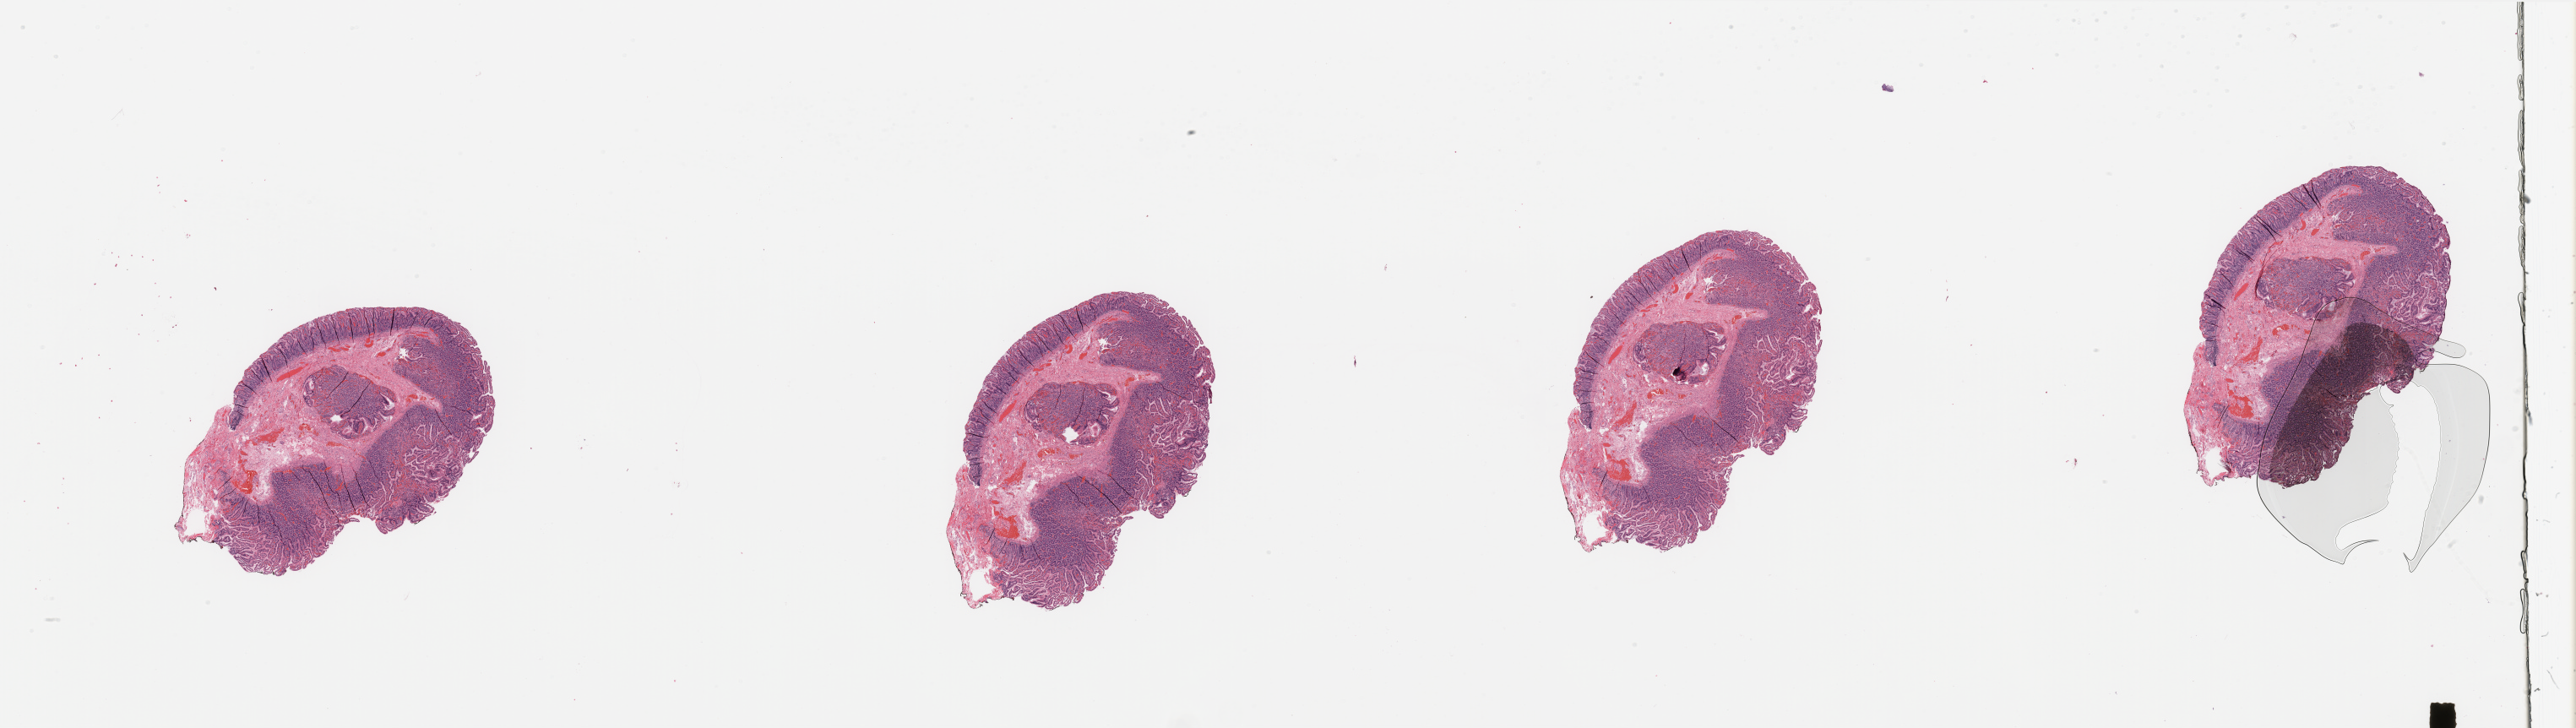
Whole-slide histology image, H&E-stained — whole scanned area (about 48.2 x 13.6 mm) shown as a low-resolution overview, normal (non-tumour) tissue sample, sampled site: pancreas. 52-year-old female patient.
* this section: normal (non-tumour) tissue from the same patient
* patient diagnosis: Infiltrating duct carcinoma, NOS